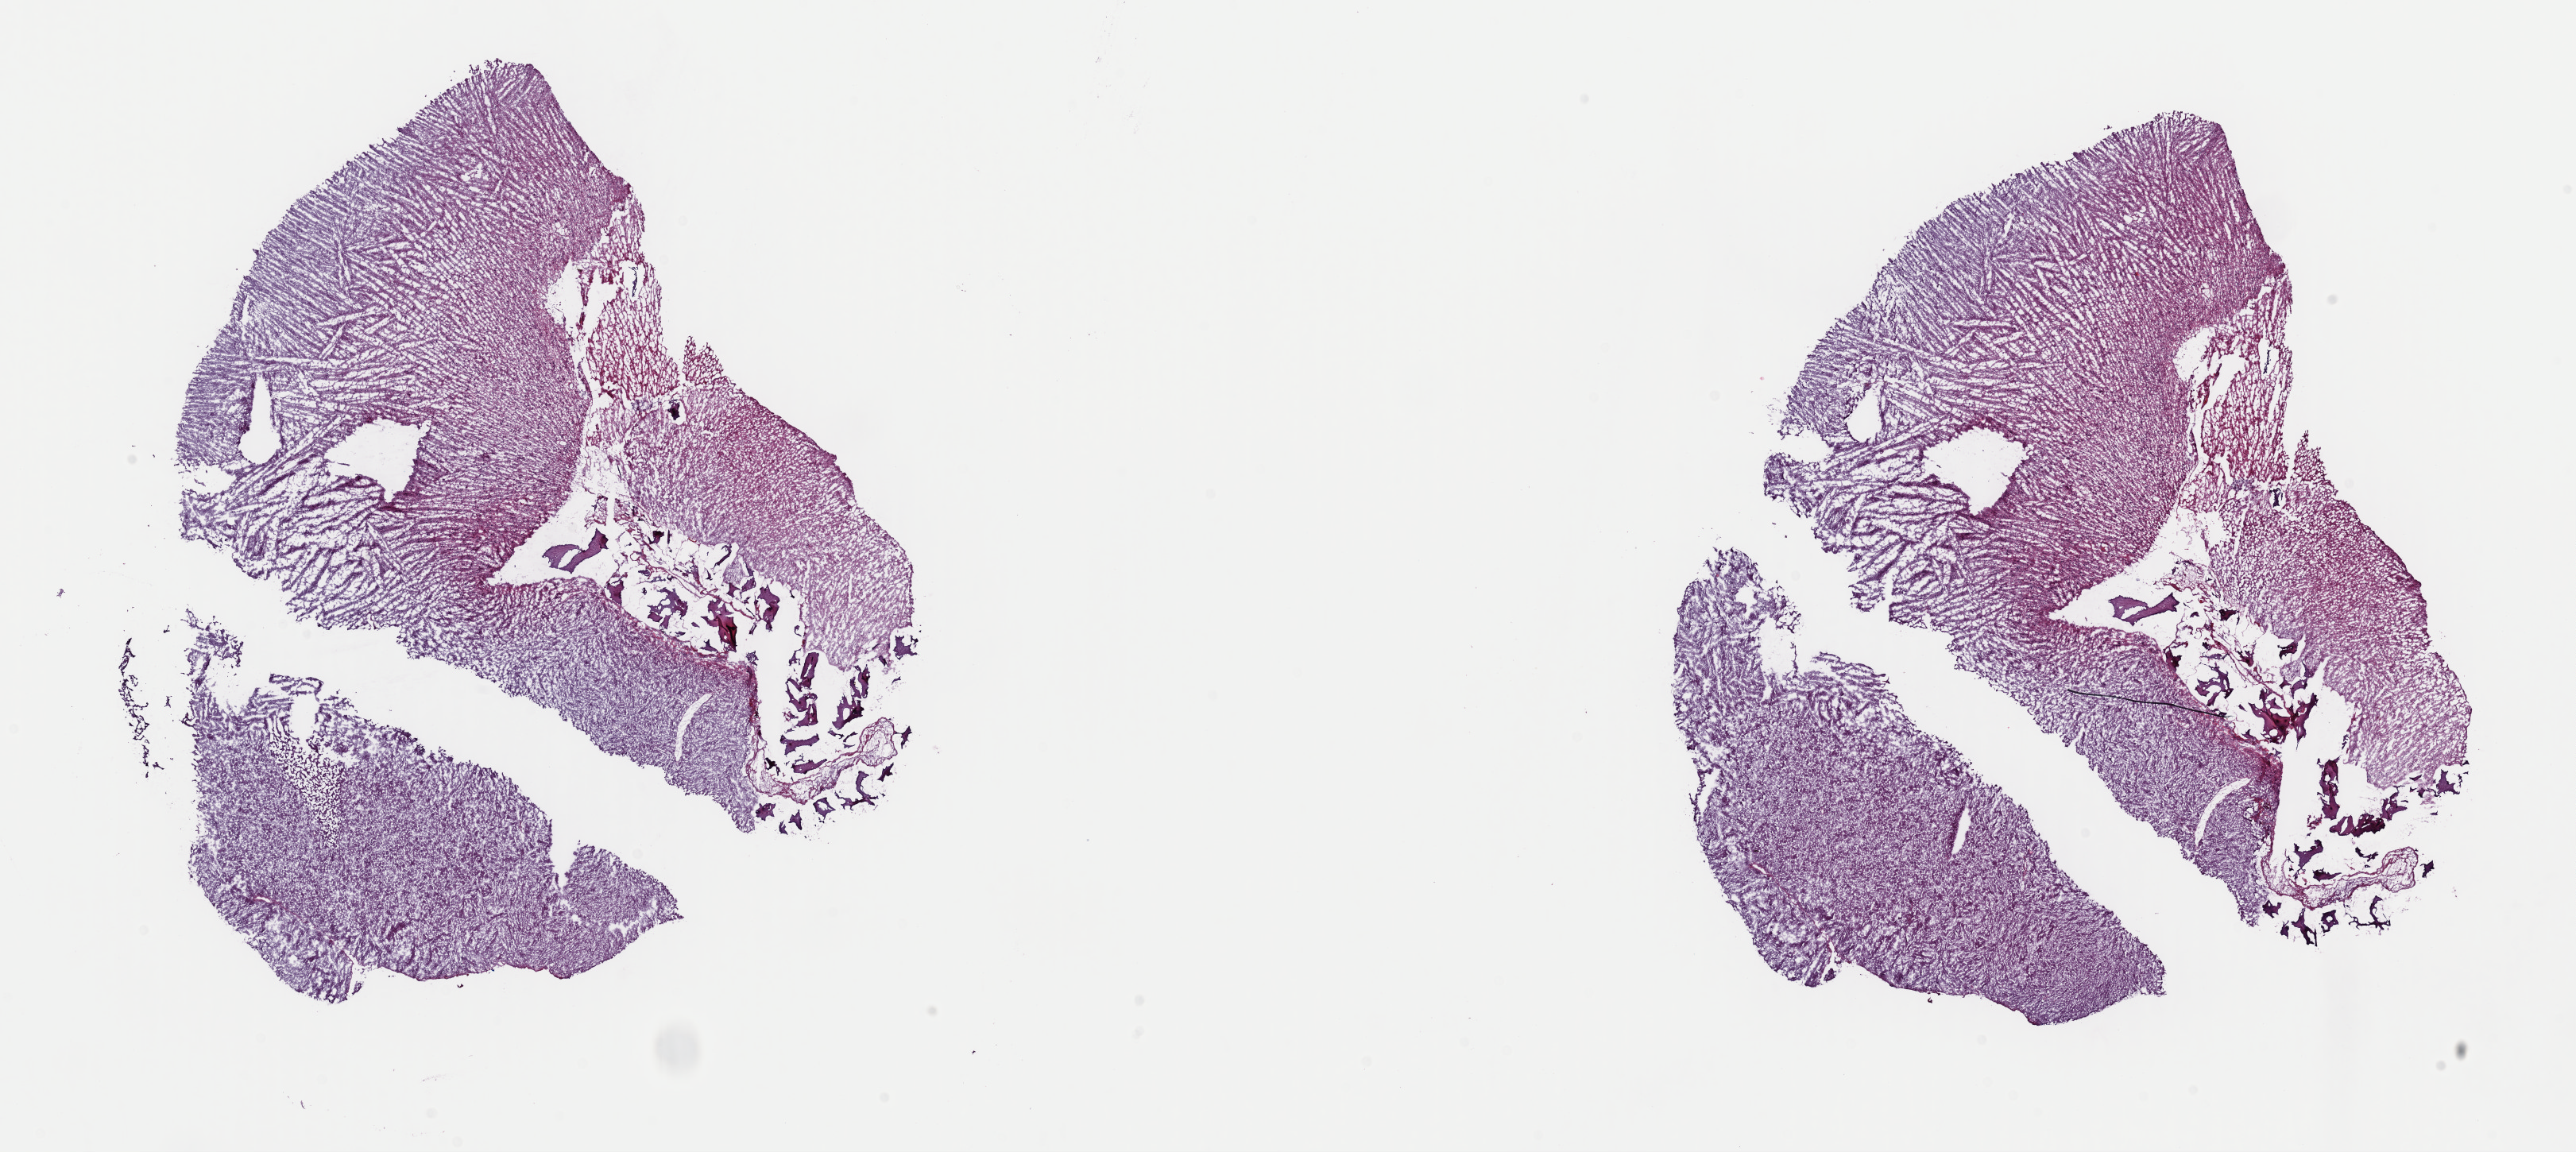
Digitized Hematoxylin and eosin (H&E) stained tissue section (whole slide) — shown as a low-resolution overview of the whole scanned area (about 25.6 x 11.5 mm), frozen section from the top of the tissue portion, recurrent tumour sample from the brain. Female patient; age at initial diagnosis 27 years. Composition of this section per pathologist review: tumour cells 70%, tumour nuclei 80%, normal cells 10%, stromal cells 20%, necrosis 0%. Inflammatory infiltration, as recorded: lymphocyte infiltration 0%, monocyte infiltration 0%, neutrophil infiltration 0%.
This section: recurrent tumour. Patient diagnosis: Oligodendroglioma, NOS (temporal lobe).